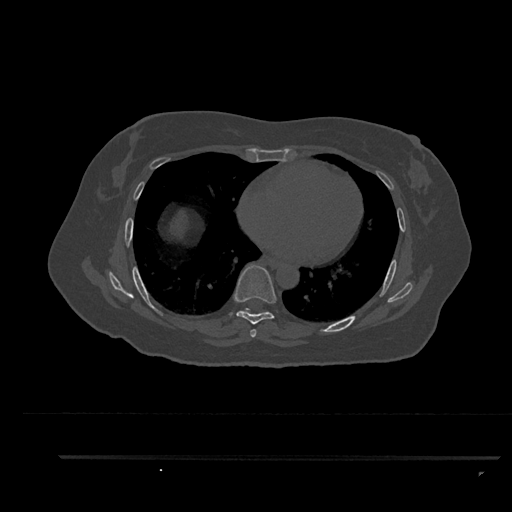
CT including the spine, one axial slice. Position 503 of 797 along the scan axis. Reconstruction kernel Br40s/3. Bone window (W 1800 / L 400 HU). 0.5 mm slice thickness. 512 × 512 image matrix. Patient: female, 44 years. Case-level facts recorded for this patient, not image findings: primary cancer: renal; vertebrae with lytic lesions (as recorded): L1.
Outlined on this slice (semi-automatically segmented with operator editing):
- T6 vertebra: box from (x=250, y=329) to (x=257, y=337) px
- T7 vertebra: (x=233, y=265)–(x=276, y=334)
- T8 vertebra: (x=242, y=308)–(x=268, y=314)